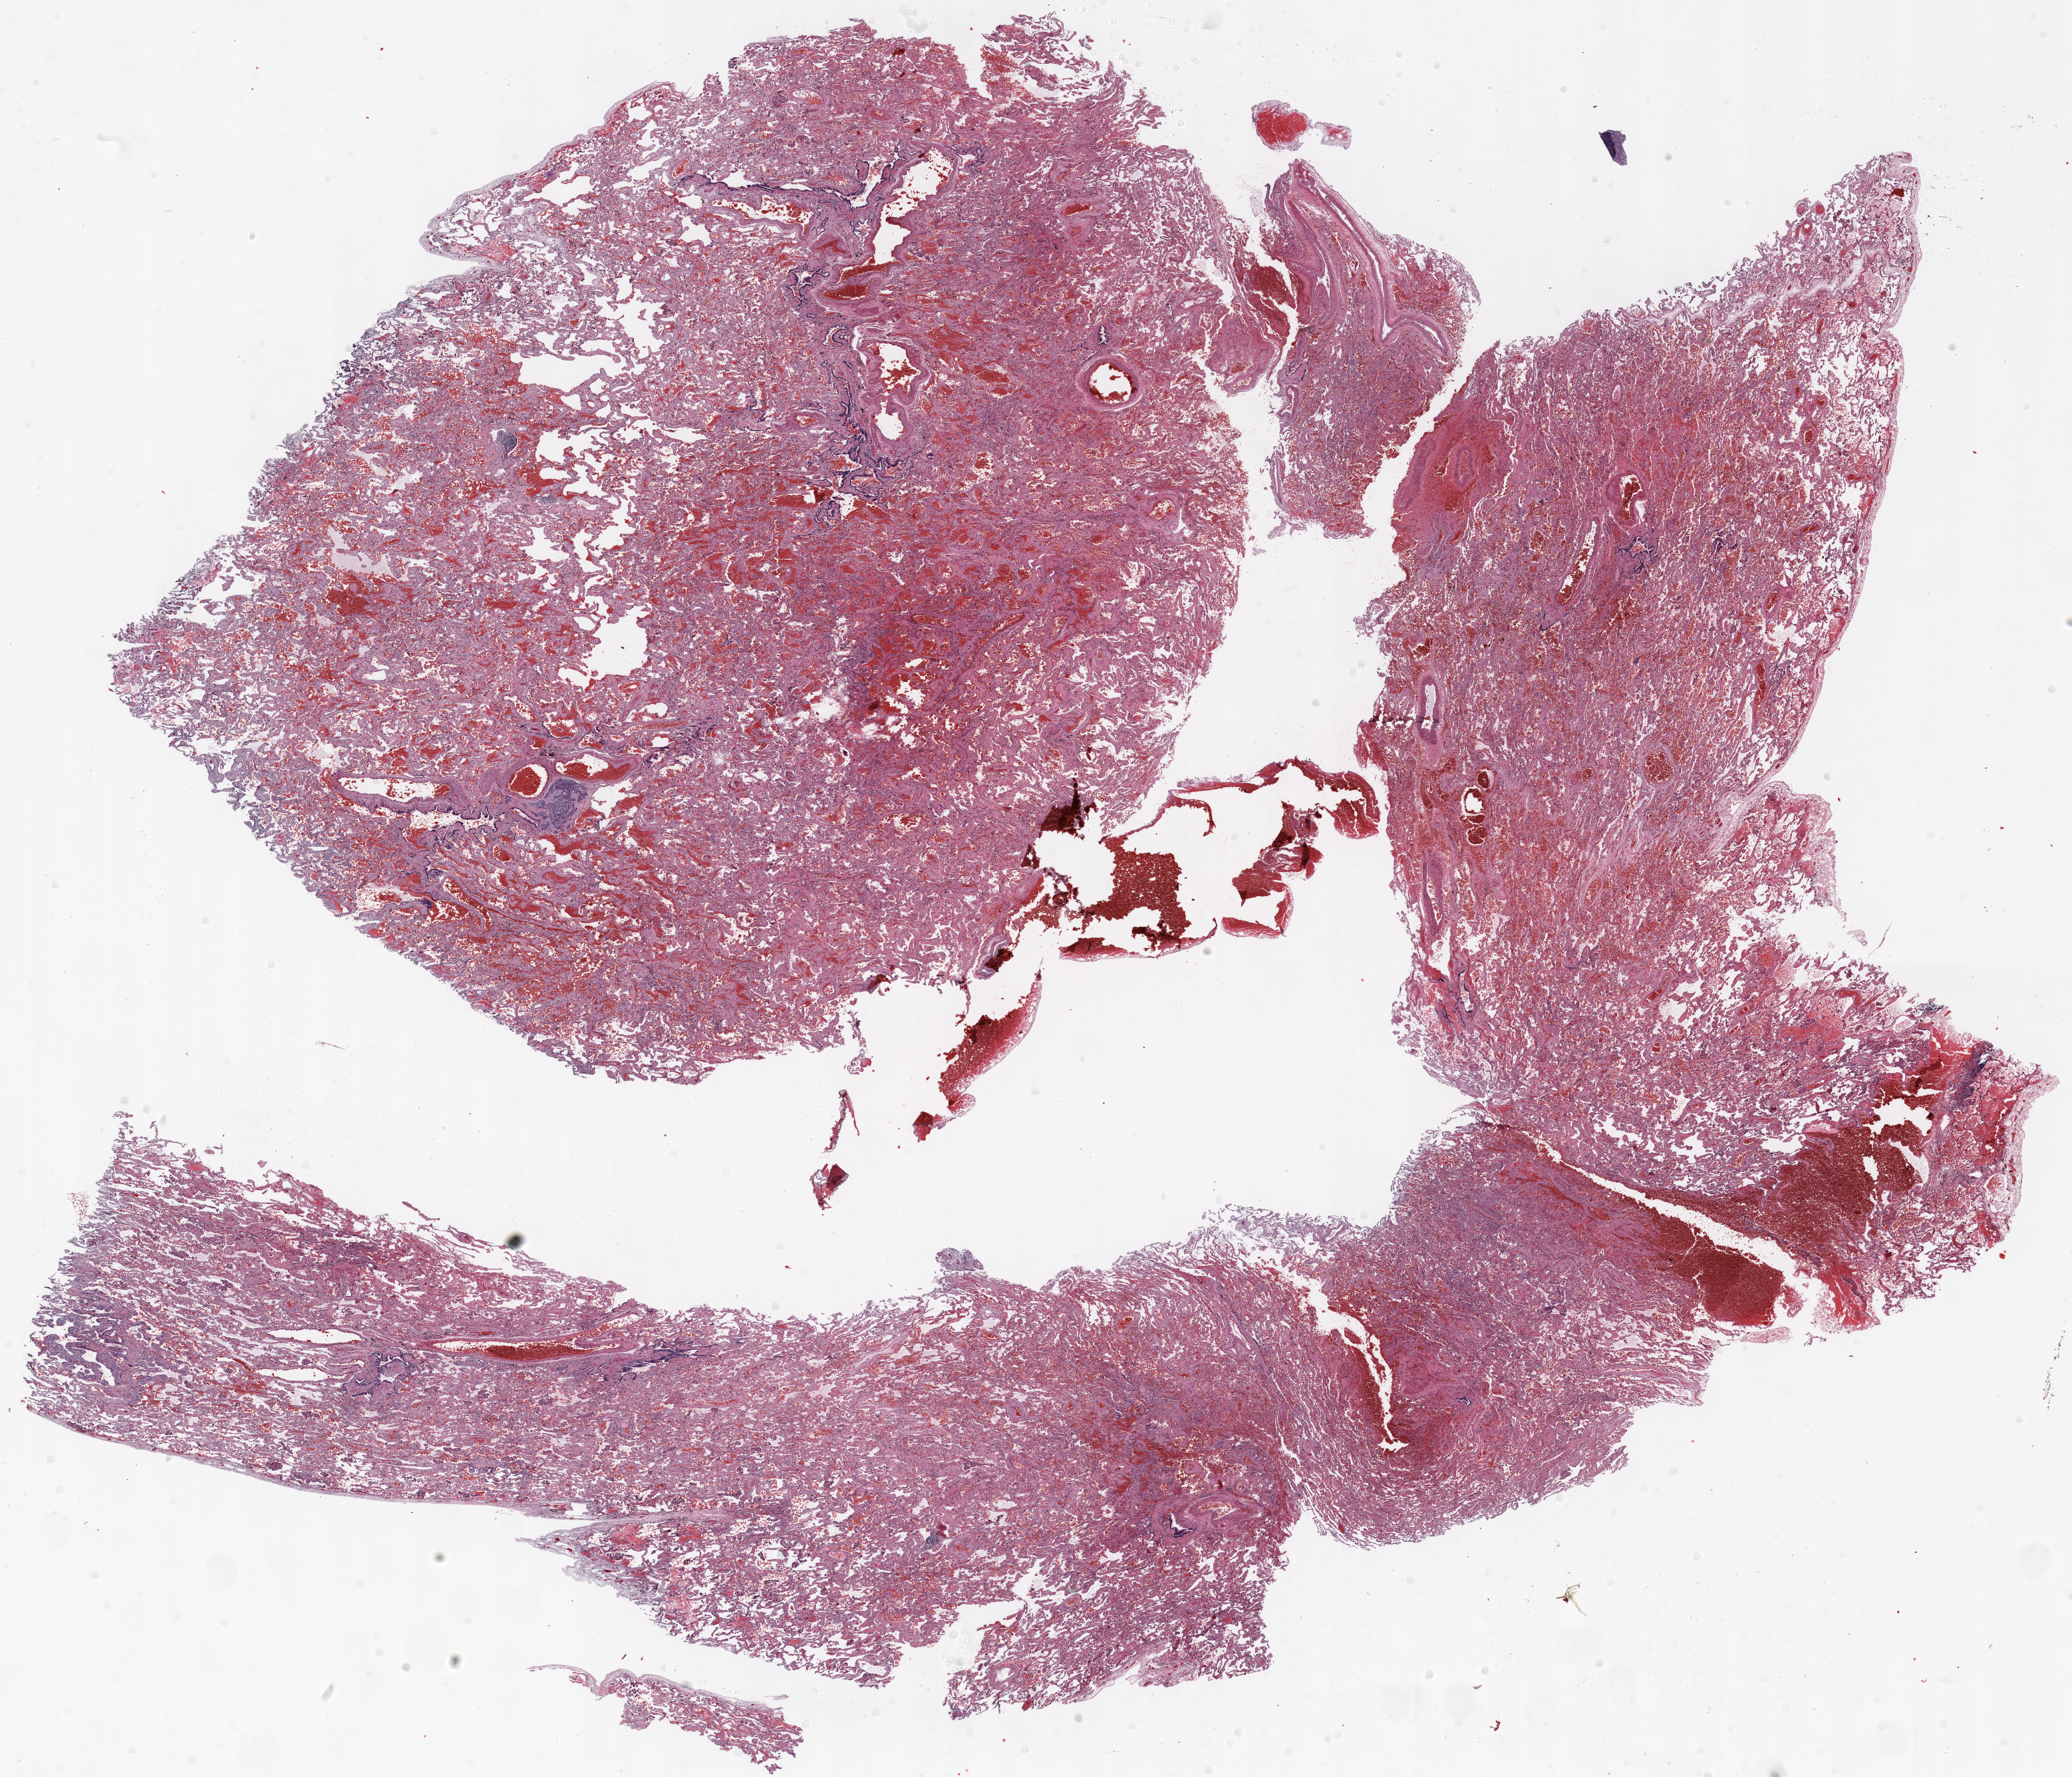
Whole-slide histology image, Hematoxylin and eosin (H&E) stained — low-resolution overview of the scanned area, about 25.0 x 21.5 mm (slide scanned at 20x), formalin-fixed paraffin-embedded (FFPE) section, lung. Female patient, aged 69 at enrolment. Current smoker at enrolment. Grade: moderately differentiated (G2).
ICD-O-3 topography: lower lobe of lung (C34.3). Stage (AJCC 6th edition): IA. Participant's lung-cancer diagnosis: Adenocarcinoma, NOS. Primary tumour location (clinical record): right lower lobe. Tumour size (pathology): 16 mm.